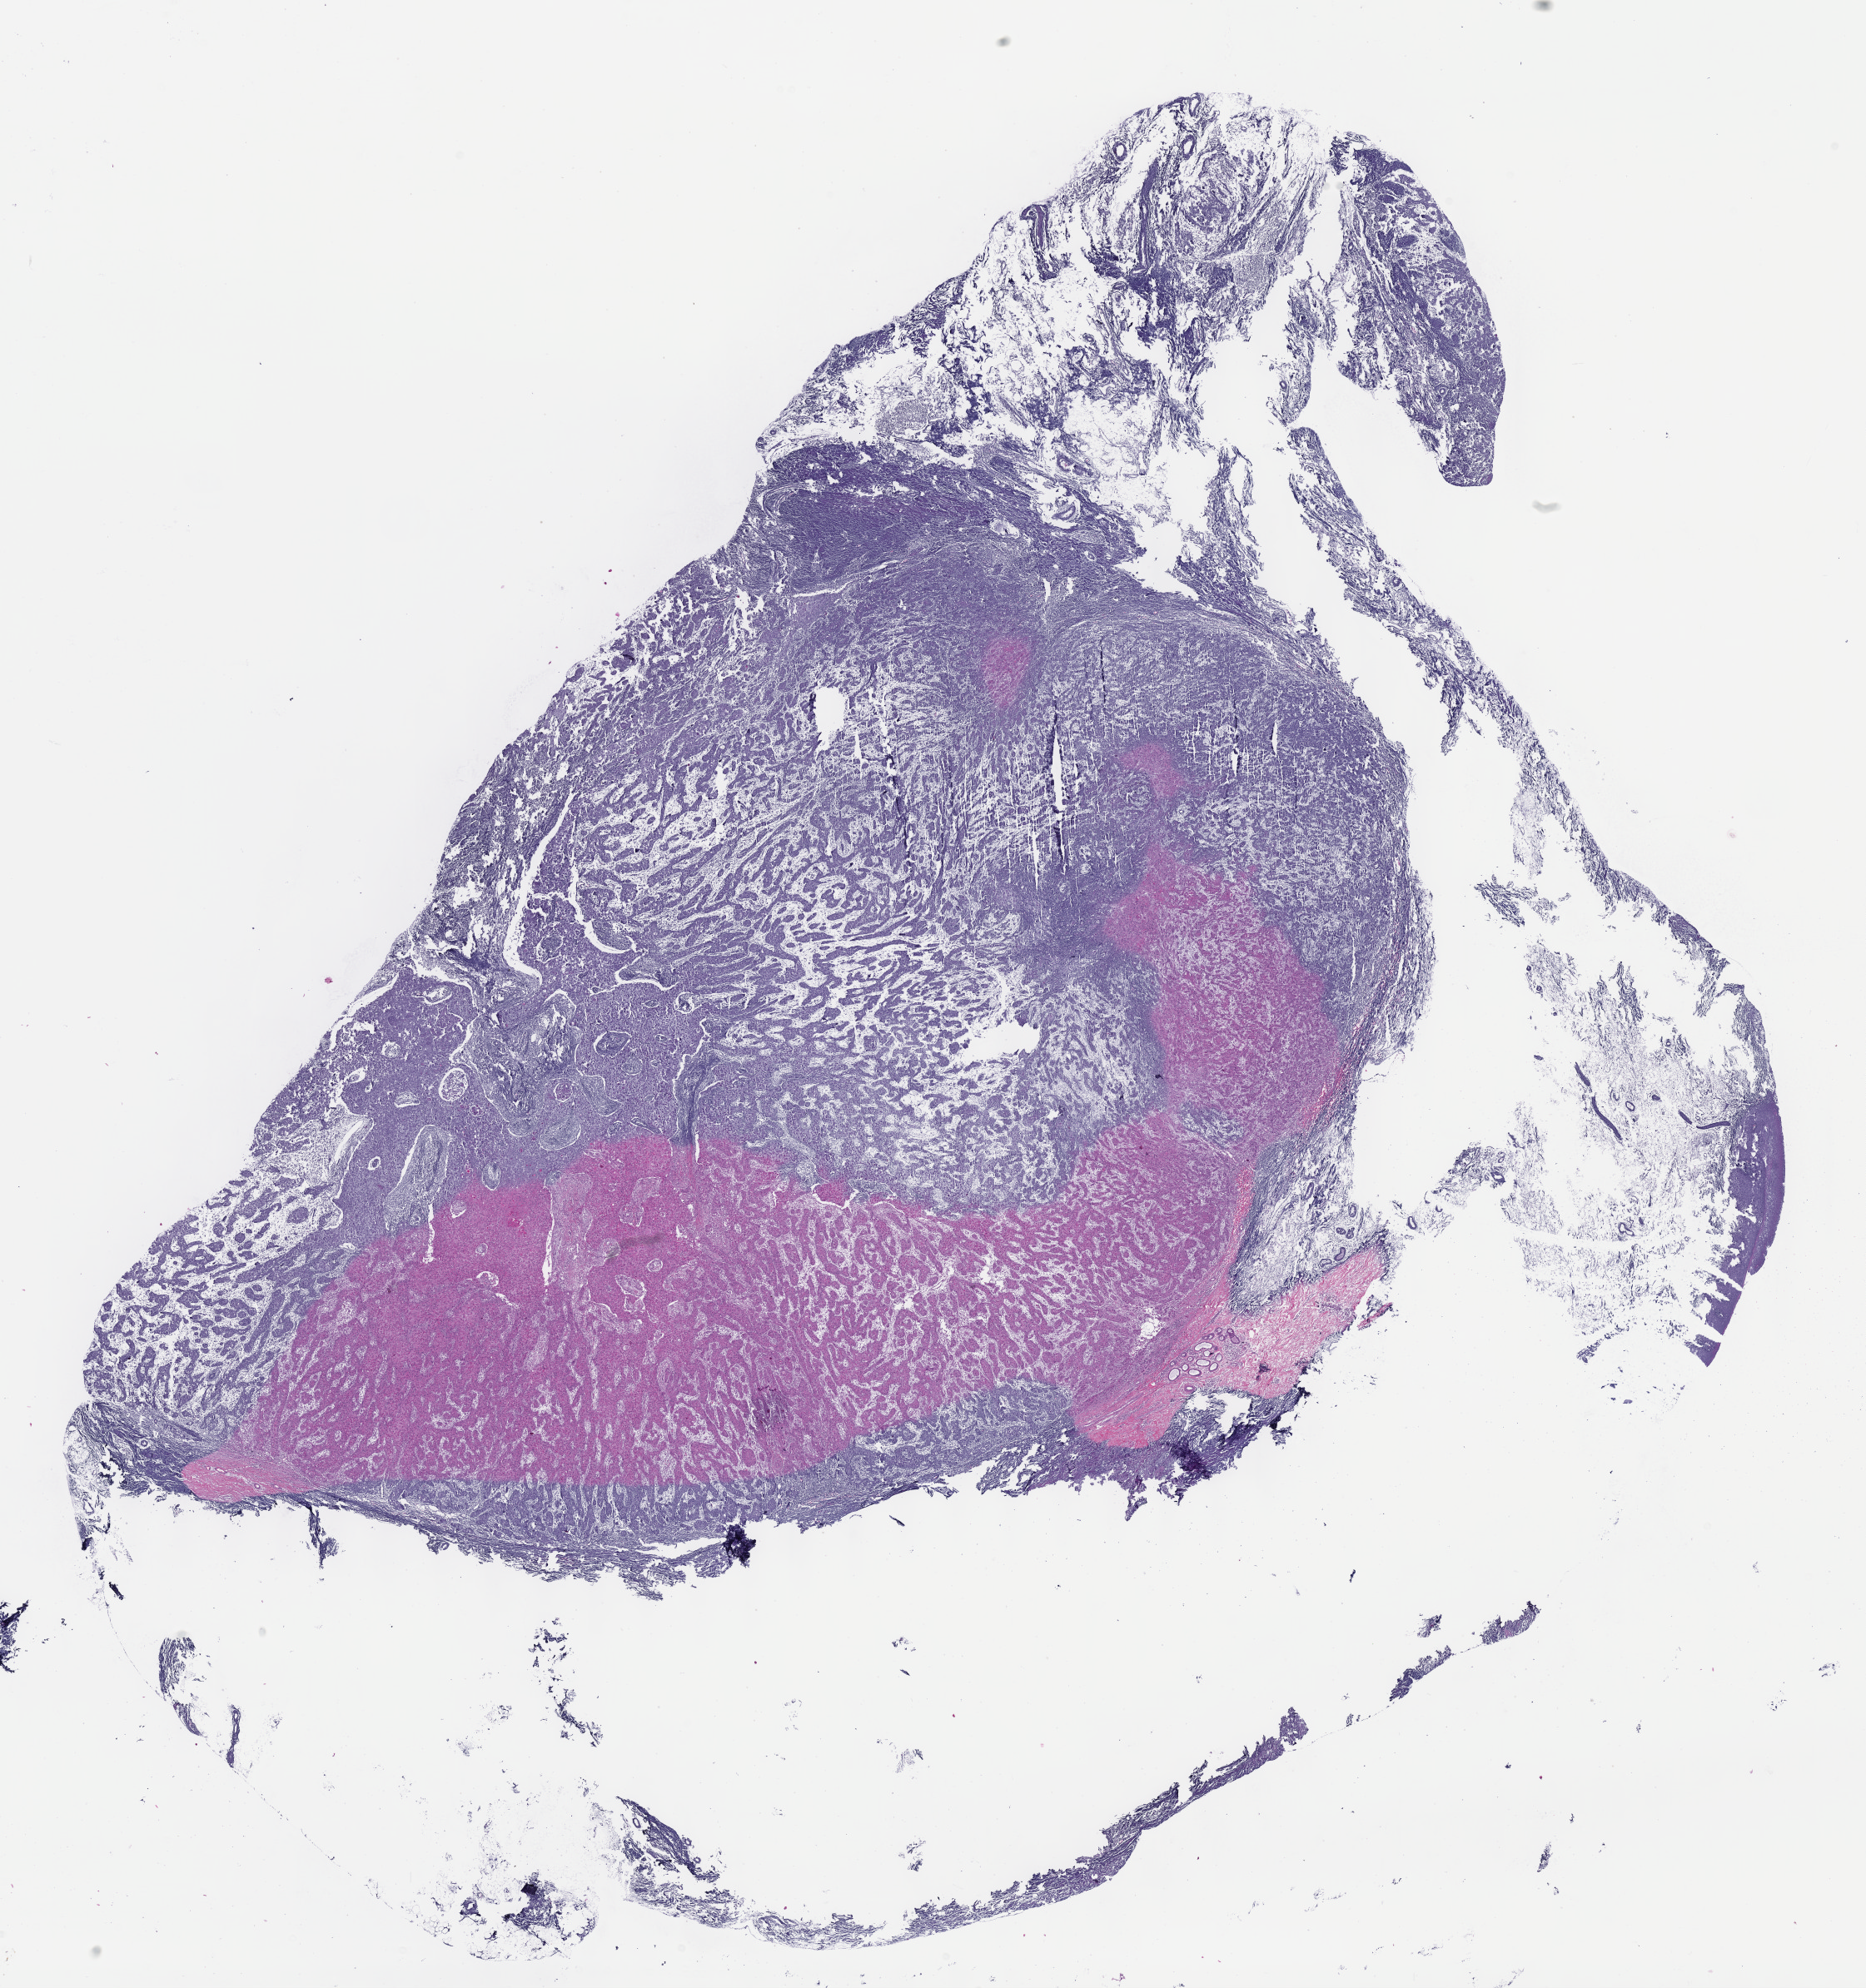
Whole-slide histology image, H&E — low-resolution overview of the scanned area, about 18.1 x 19.3 mm (acquisition: 40x scan); formalin-fixed paraffin-embedded (FFPE) diagnostic section; sample: primary tumour, head and neck. Male, age 64 years at initial diagnosis. Histologic grade: G2 (moderately differentiated).
Pathologic diagnosis: Squamous cell carcinoma, NOS (overlapping lesion of lip, oral cavity and pharynx). AJCC pathologic stage: IVA (7th edition). Laterality: left.